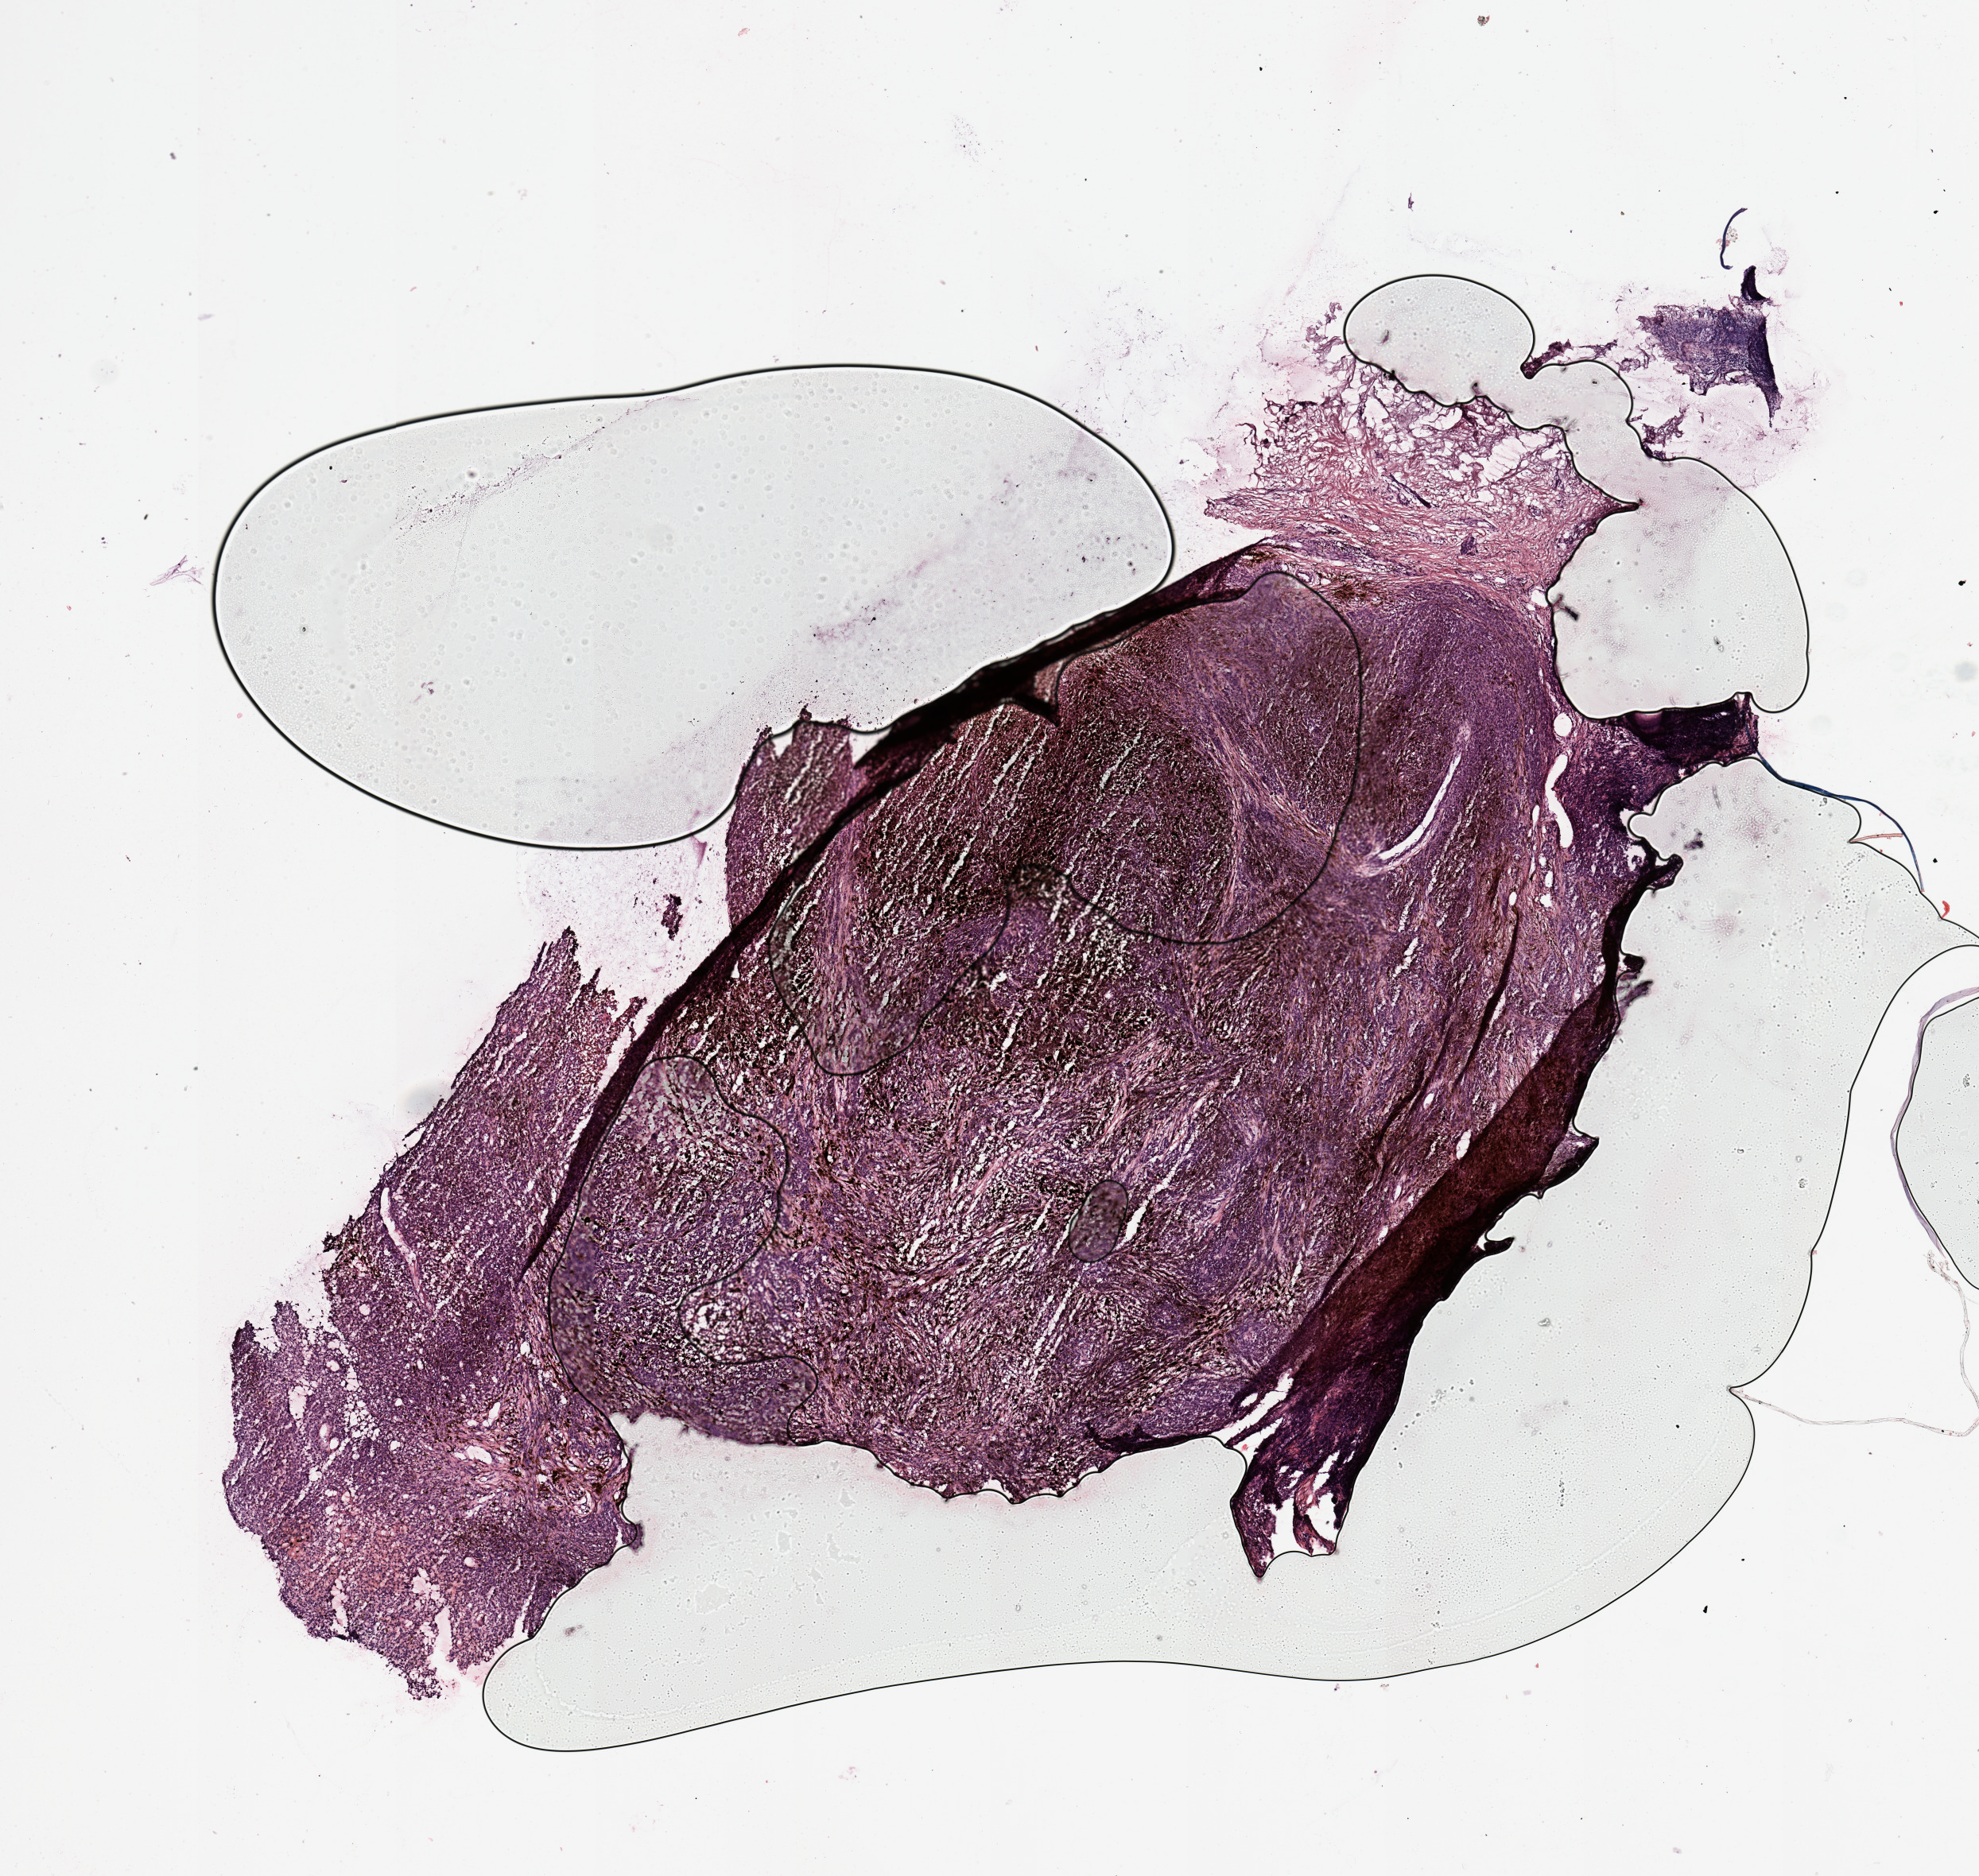
H&E-stained whole-slide image, shown as a low-resolution overview of the whole scanned area (about 9.8 x 9.3 mm, acquisition: 20x scan); melanoma tumour tissue; sampled site not recorded. Female, 53 y/o.
Patient diagnosis (cohort enrolment): cutaneous melanoma (skin). Primary tumour site (as recorded): trunk.